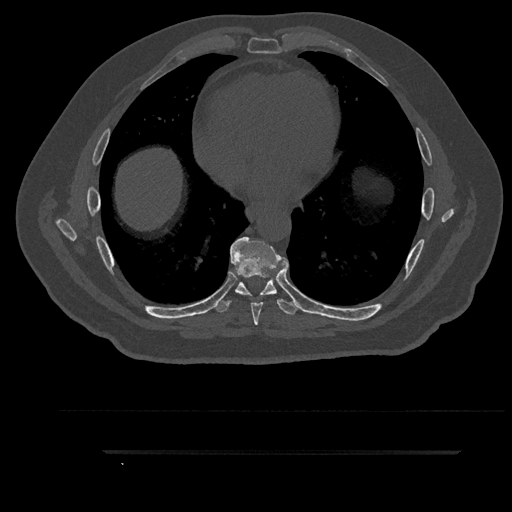
CT including the spine, one axial slice. Position 502 of 797 along the scan axis. Reconstruction kernel Br40s/3. 120 kVp. Bone window (W 1800 / L 400 HU). 0.5 mm slice thickness. 512 × 512 image matrix, field of view 432 × 432 mm. Male patient, age 63 years. Case-level facts recorded for this patient, not image findings: primary cancer: renal; vertebrae with lytic lesions (as recorded): T8.
Annotated regions visible in this slice (semi-automatically segmented with operator editing):
- T6 vertebra: box from (x=251, y=292) to (x=269, y=296) px
- T7 vertebra: (x=230, y=236)–(x=288, y=325)
- T8 vertebra: (x=214, y=250)–(x=300, y=315)